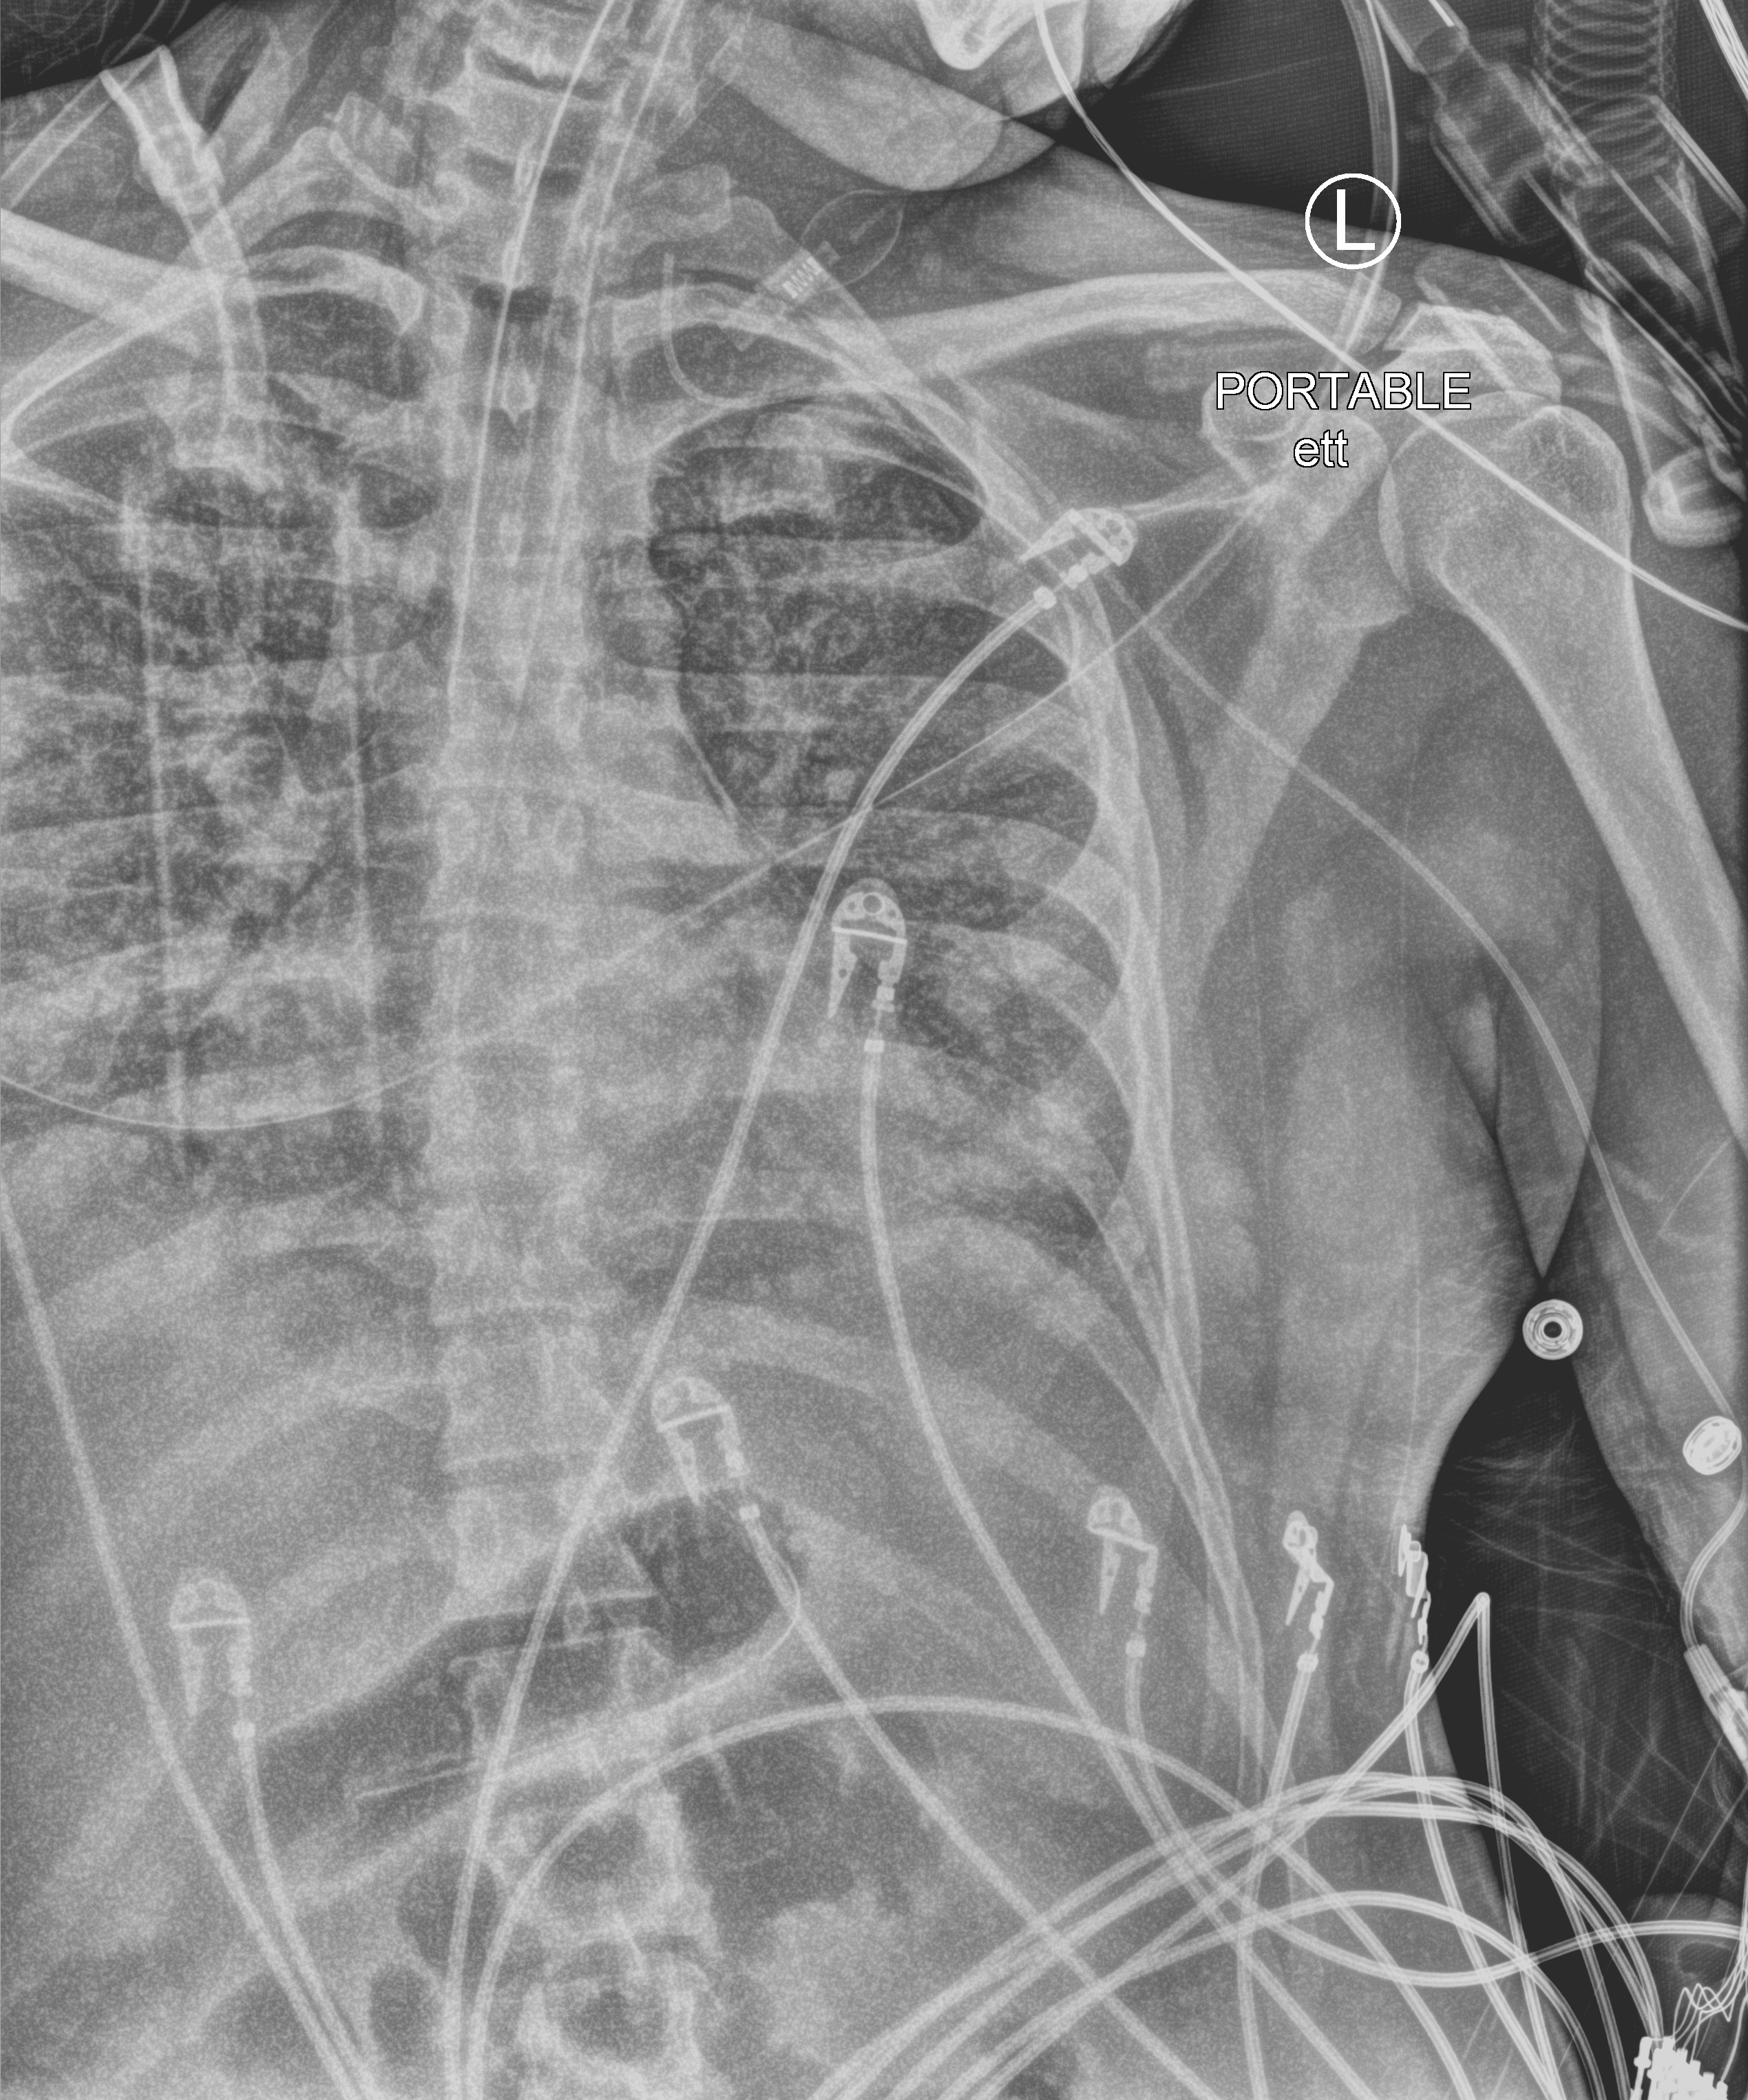
Bedside chest radiograph (computed radiography); anteroposterior (AP) projection. Male patient hospitalised with COVID-19, age 18–59 years.
Admission-level facts for this patient (not findings on this image; timing relative to this image not recorded): mechanically ventilated during this hospital stay: yes.